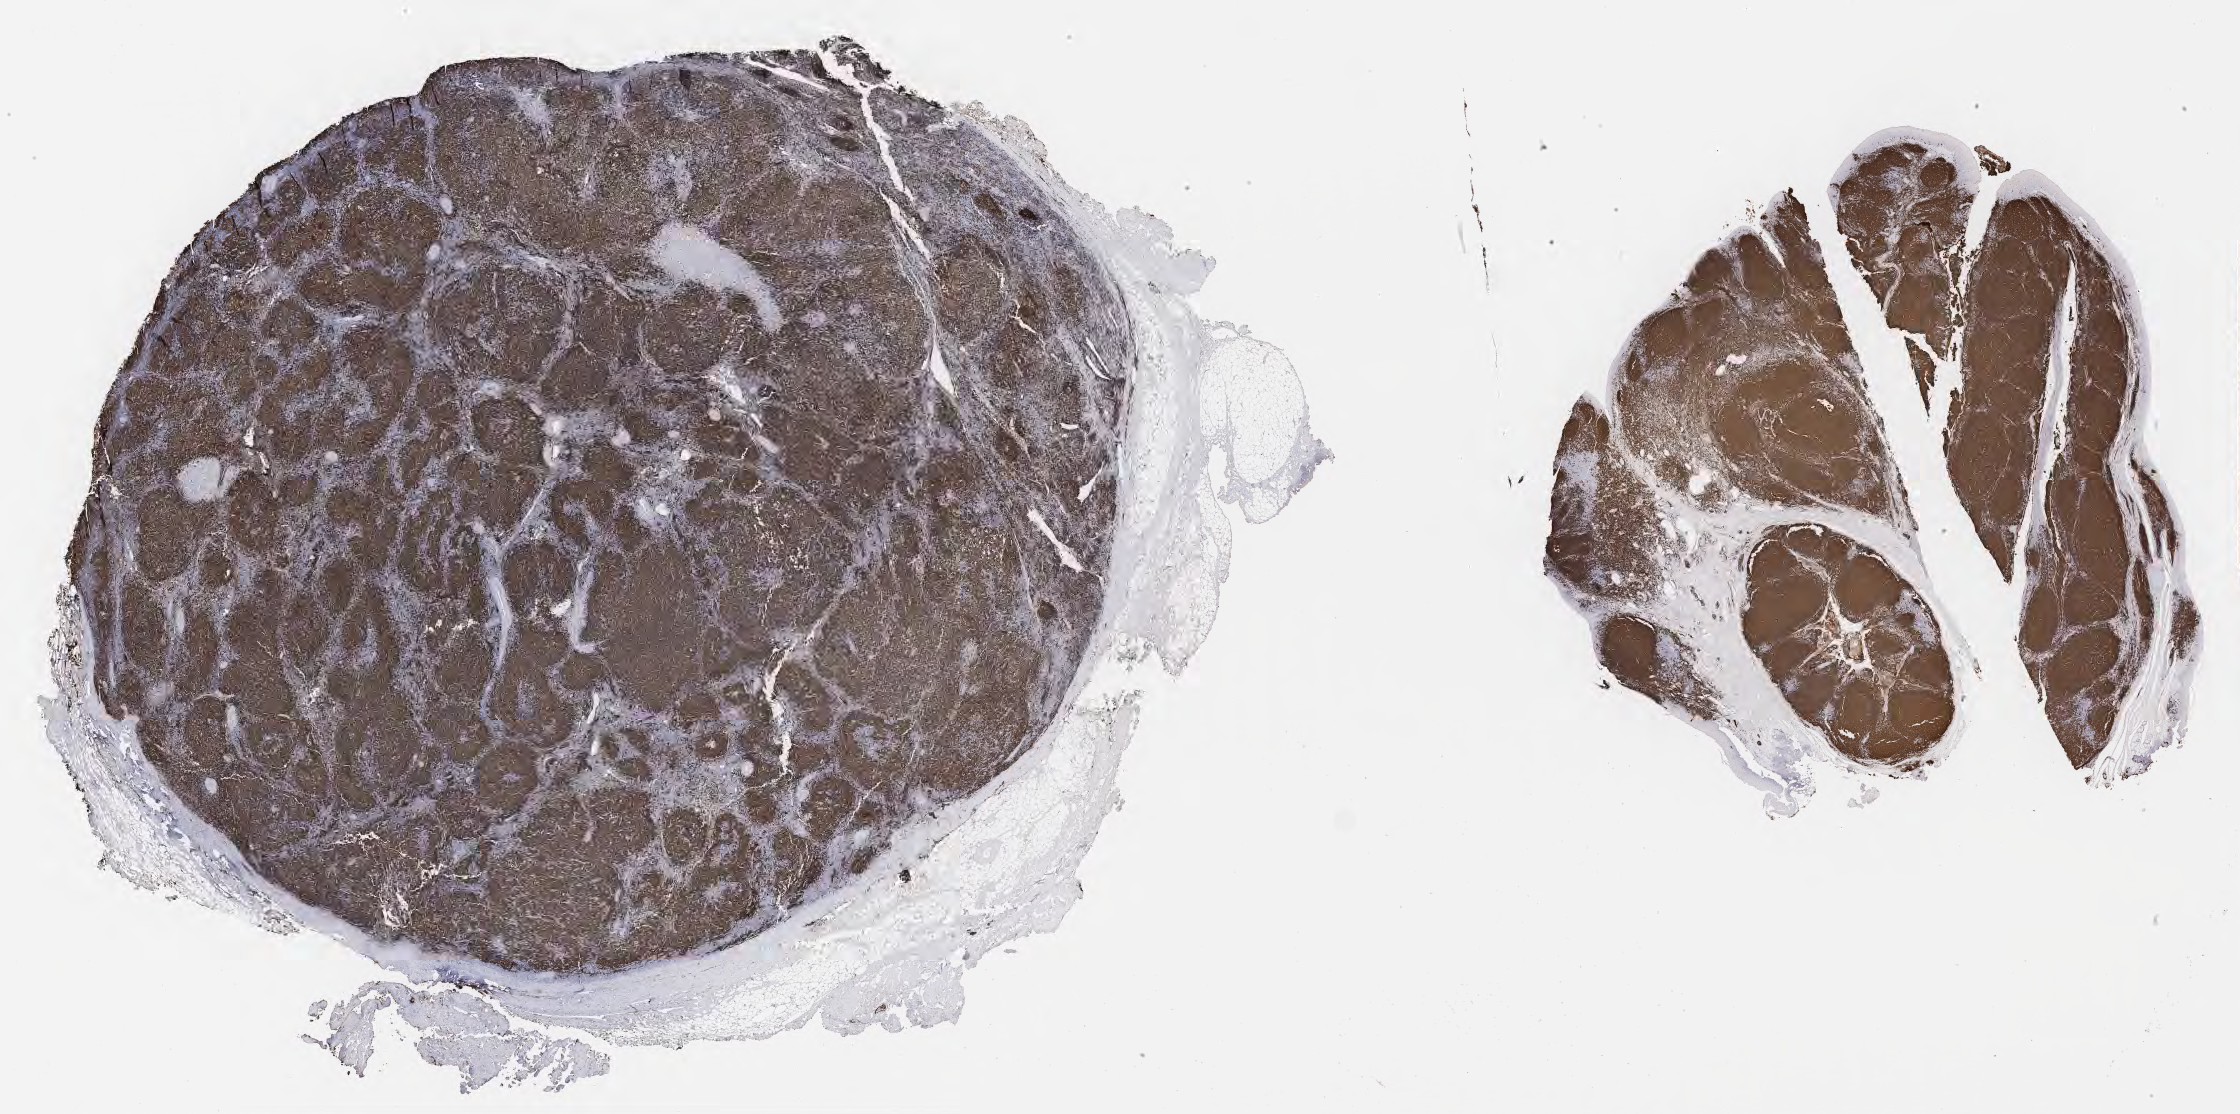
Immunohistochemistry (IHC) whole-slide image stained for CD20, shown as a low-resolution overview of the whole scanned area (about 36.2 x 18.0 mm). Tumor tissue. Site: lymph node. Male patient, age 46 years.
• histologic diagnosis: Diffuse large B-cell lymphoma, NOS